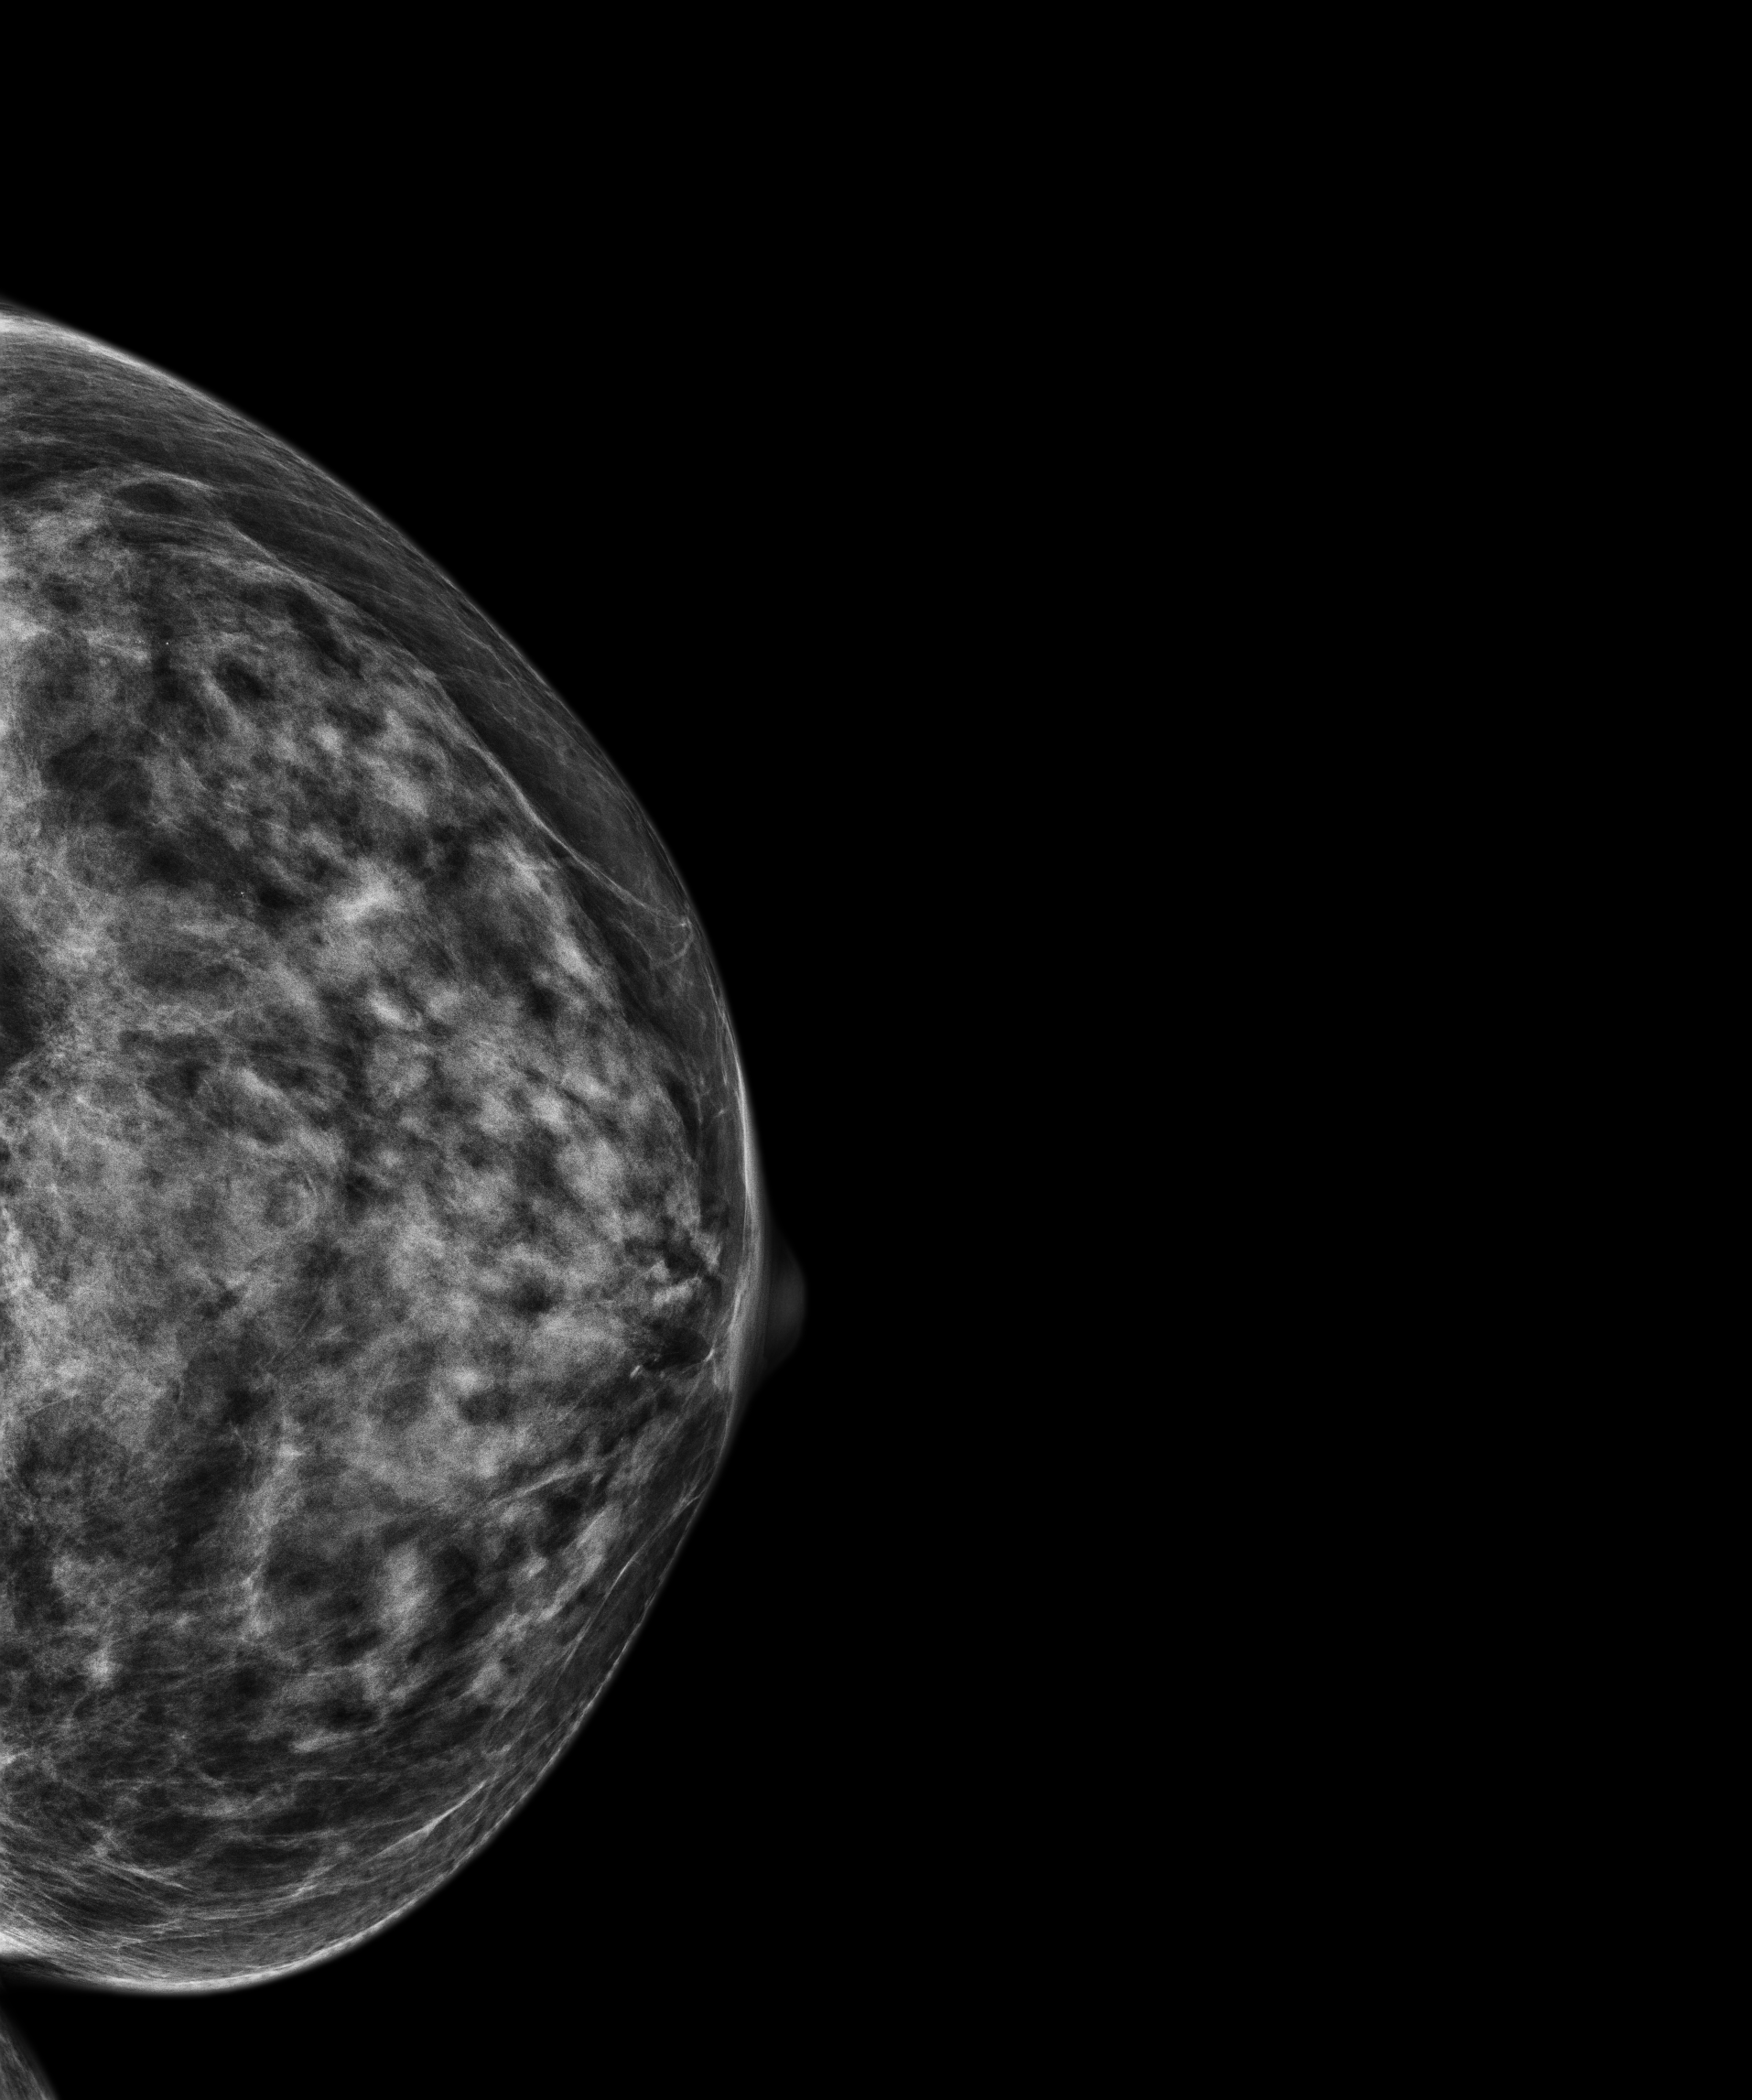
Full-field digital mammogram (FFDM), left breast, cranio-caudal projection, annual screening mammography examination, compressed breast thickness 42.6 mm, system: Senographe Pristina. Patient: female, 73 years.
BI-RADS breast density category at the screening exam (both breasts, scale 1–4): 4. Final BI-RADS category for the screening round (tomosynthesis exam, both breasts): category 1. Recall: no recall after this screen.